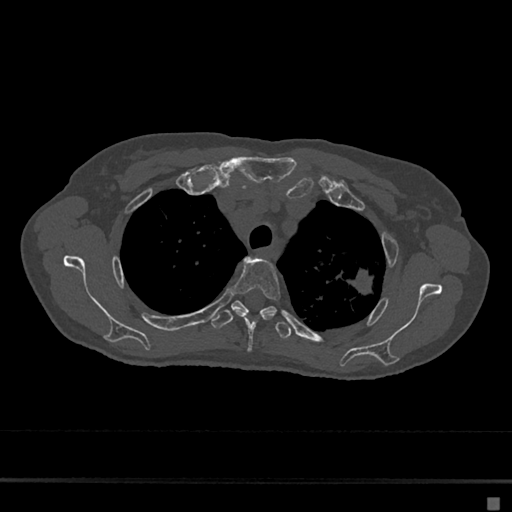
CT including the spine, one axial slice. Slice 527 of 797 in the series (ordered by position). Reconstruction kernel Br40s/3. 120 kVp. Bone window (W 1800 / L 400 HU). 512 × 512 image matrix, field of view 360 × 360 mm. Female patient, age 68 years. From the clinical record (not read from this slice): primary cancer: renal.
Structures marked on this image (semi-automatically segmented with operator editing):
- T3 vertebra: bounding box <231,258,280,351> (left, top, right, bottom; pixels)
- T4 vertebra: <211,300,291,339>